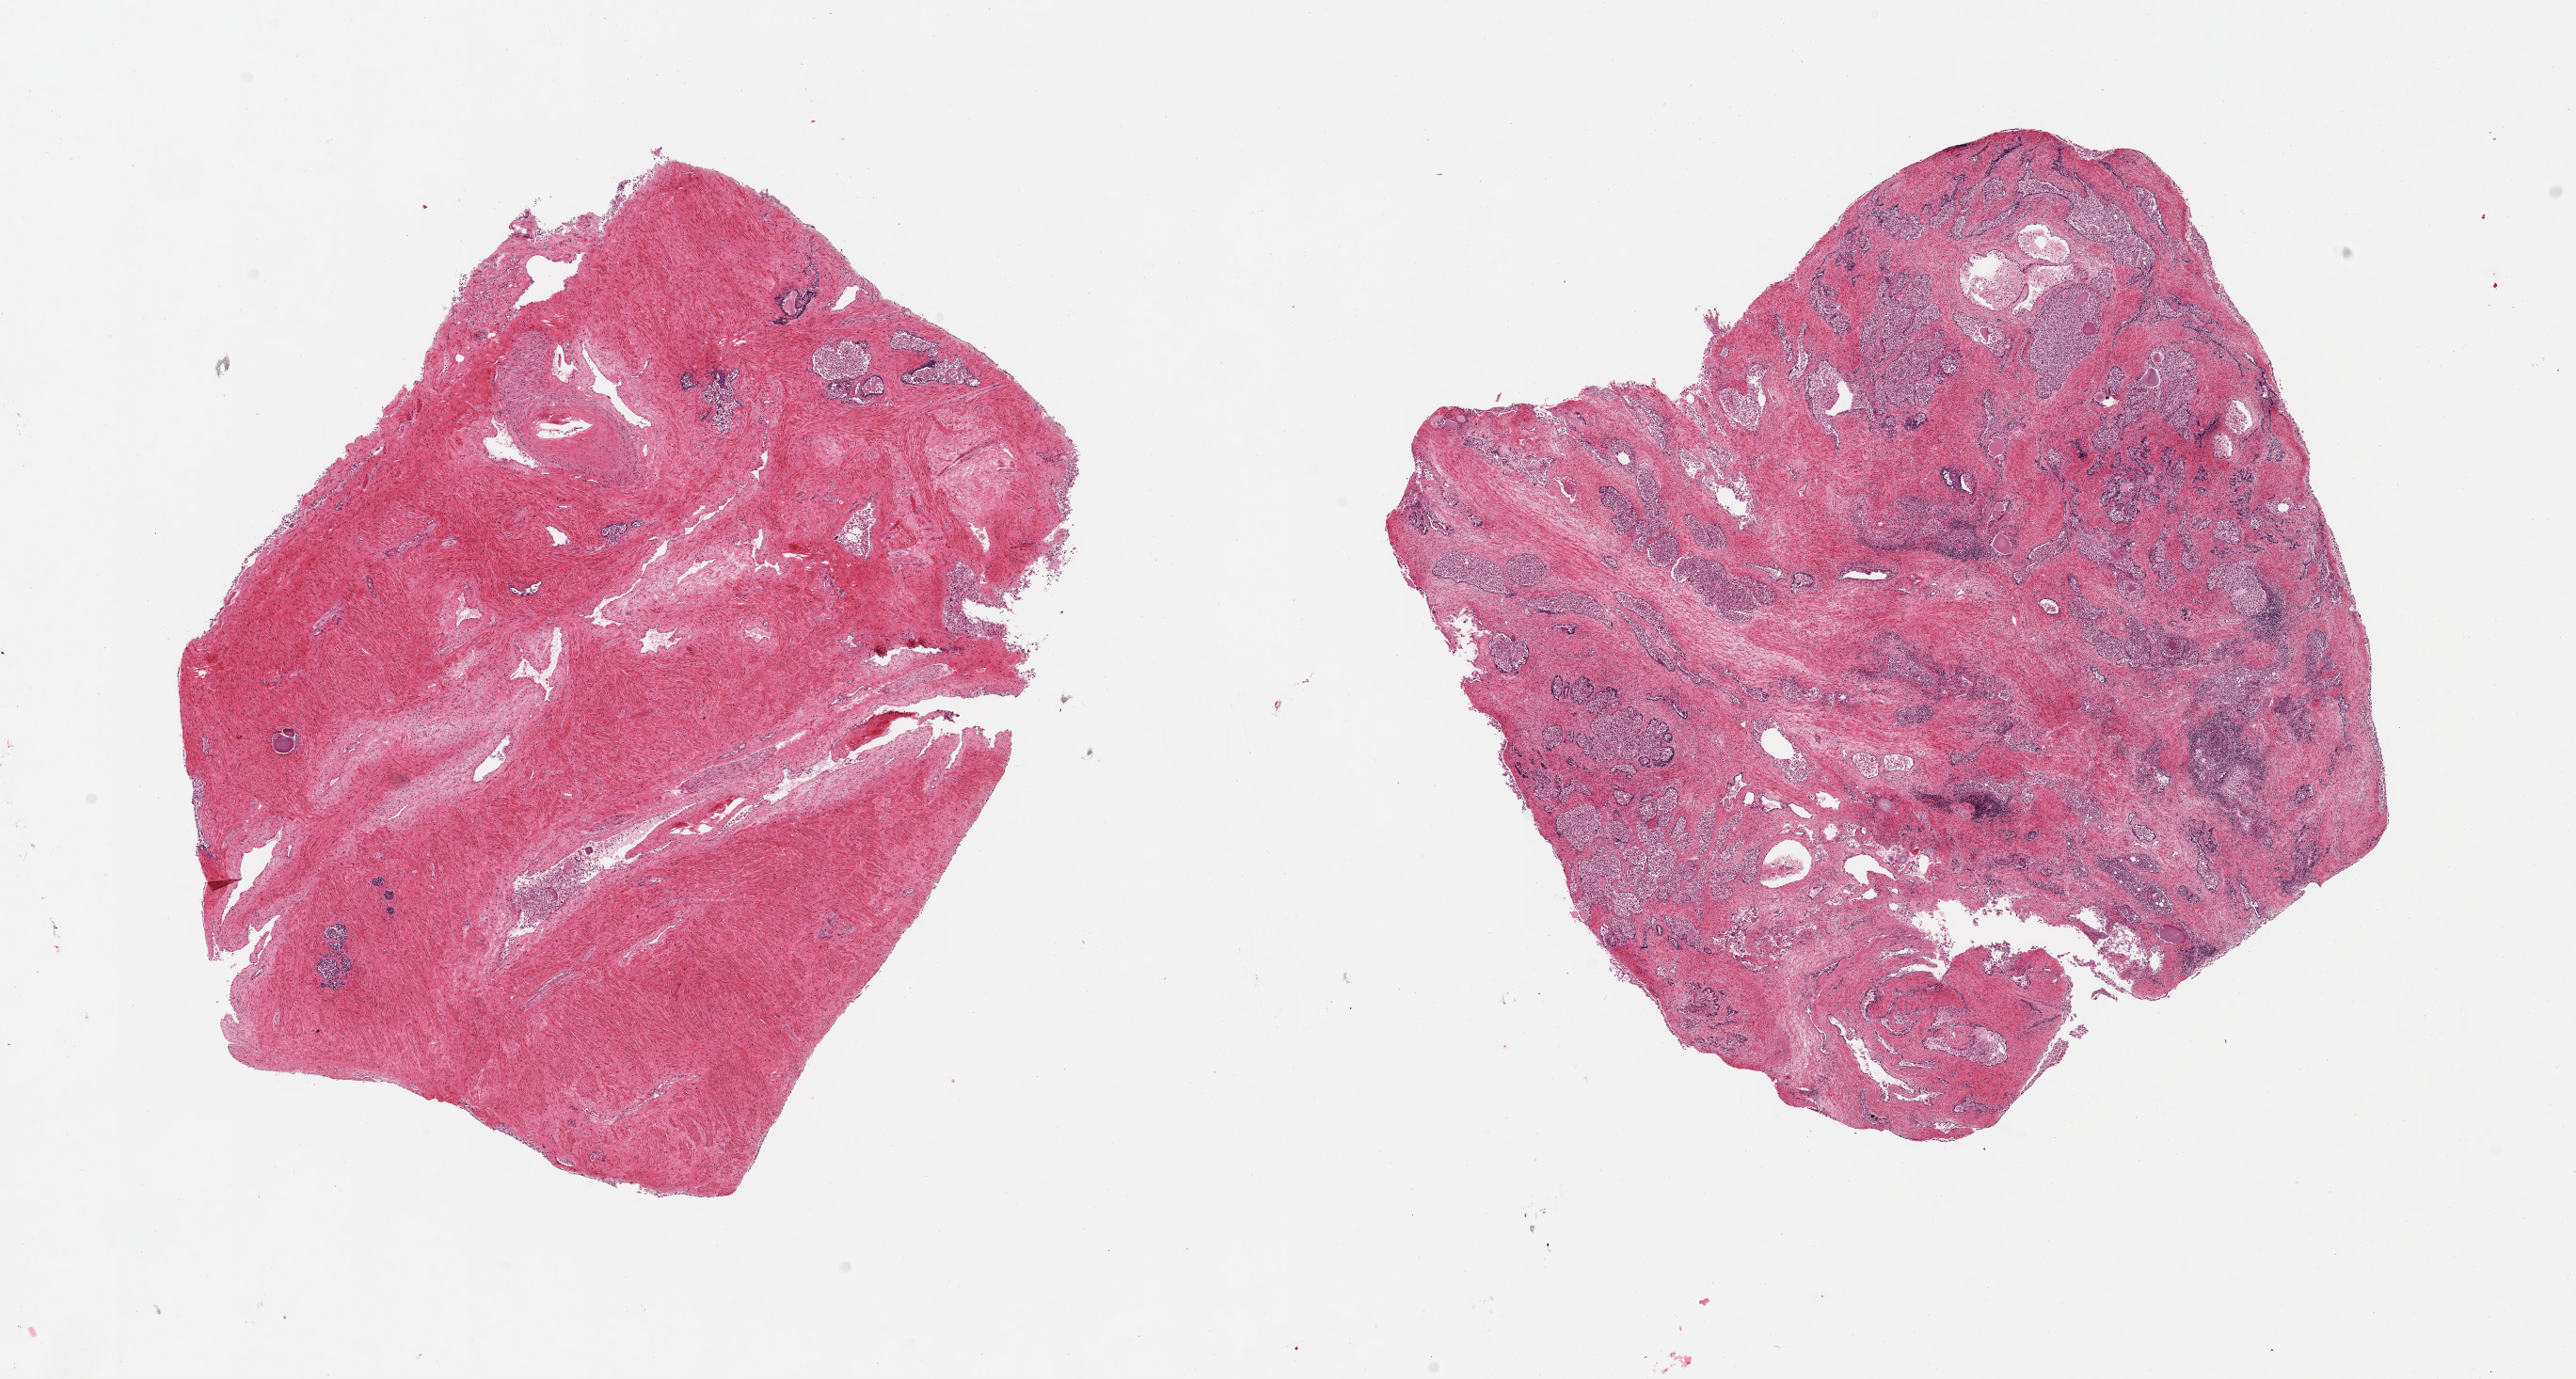
Hematoxylin and eosin (H&E) whole-slide image, brightfield, whole scanned area (about 21.7 x 11.6 mm) shown as a low-resolution overview. PAXgene-fixed paraffin-embedded (PFPE) section. Section of prostate (target tissue). Donor tissue sample. Male donor.
- review note (as recorded): 2 pieces, glanudlar autolysis